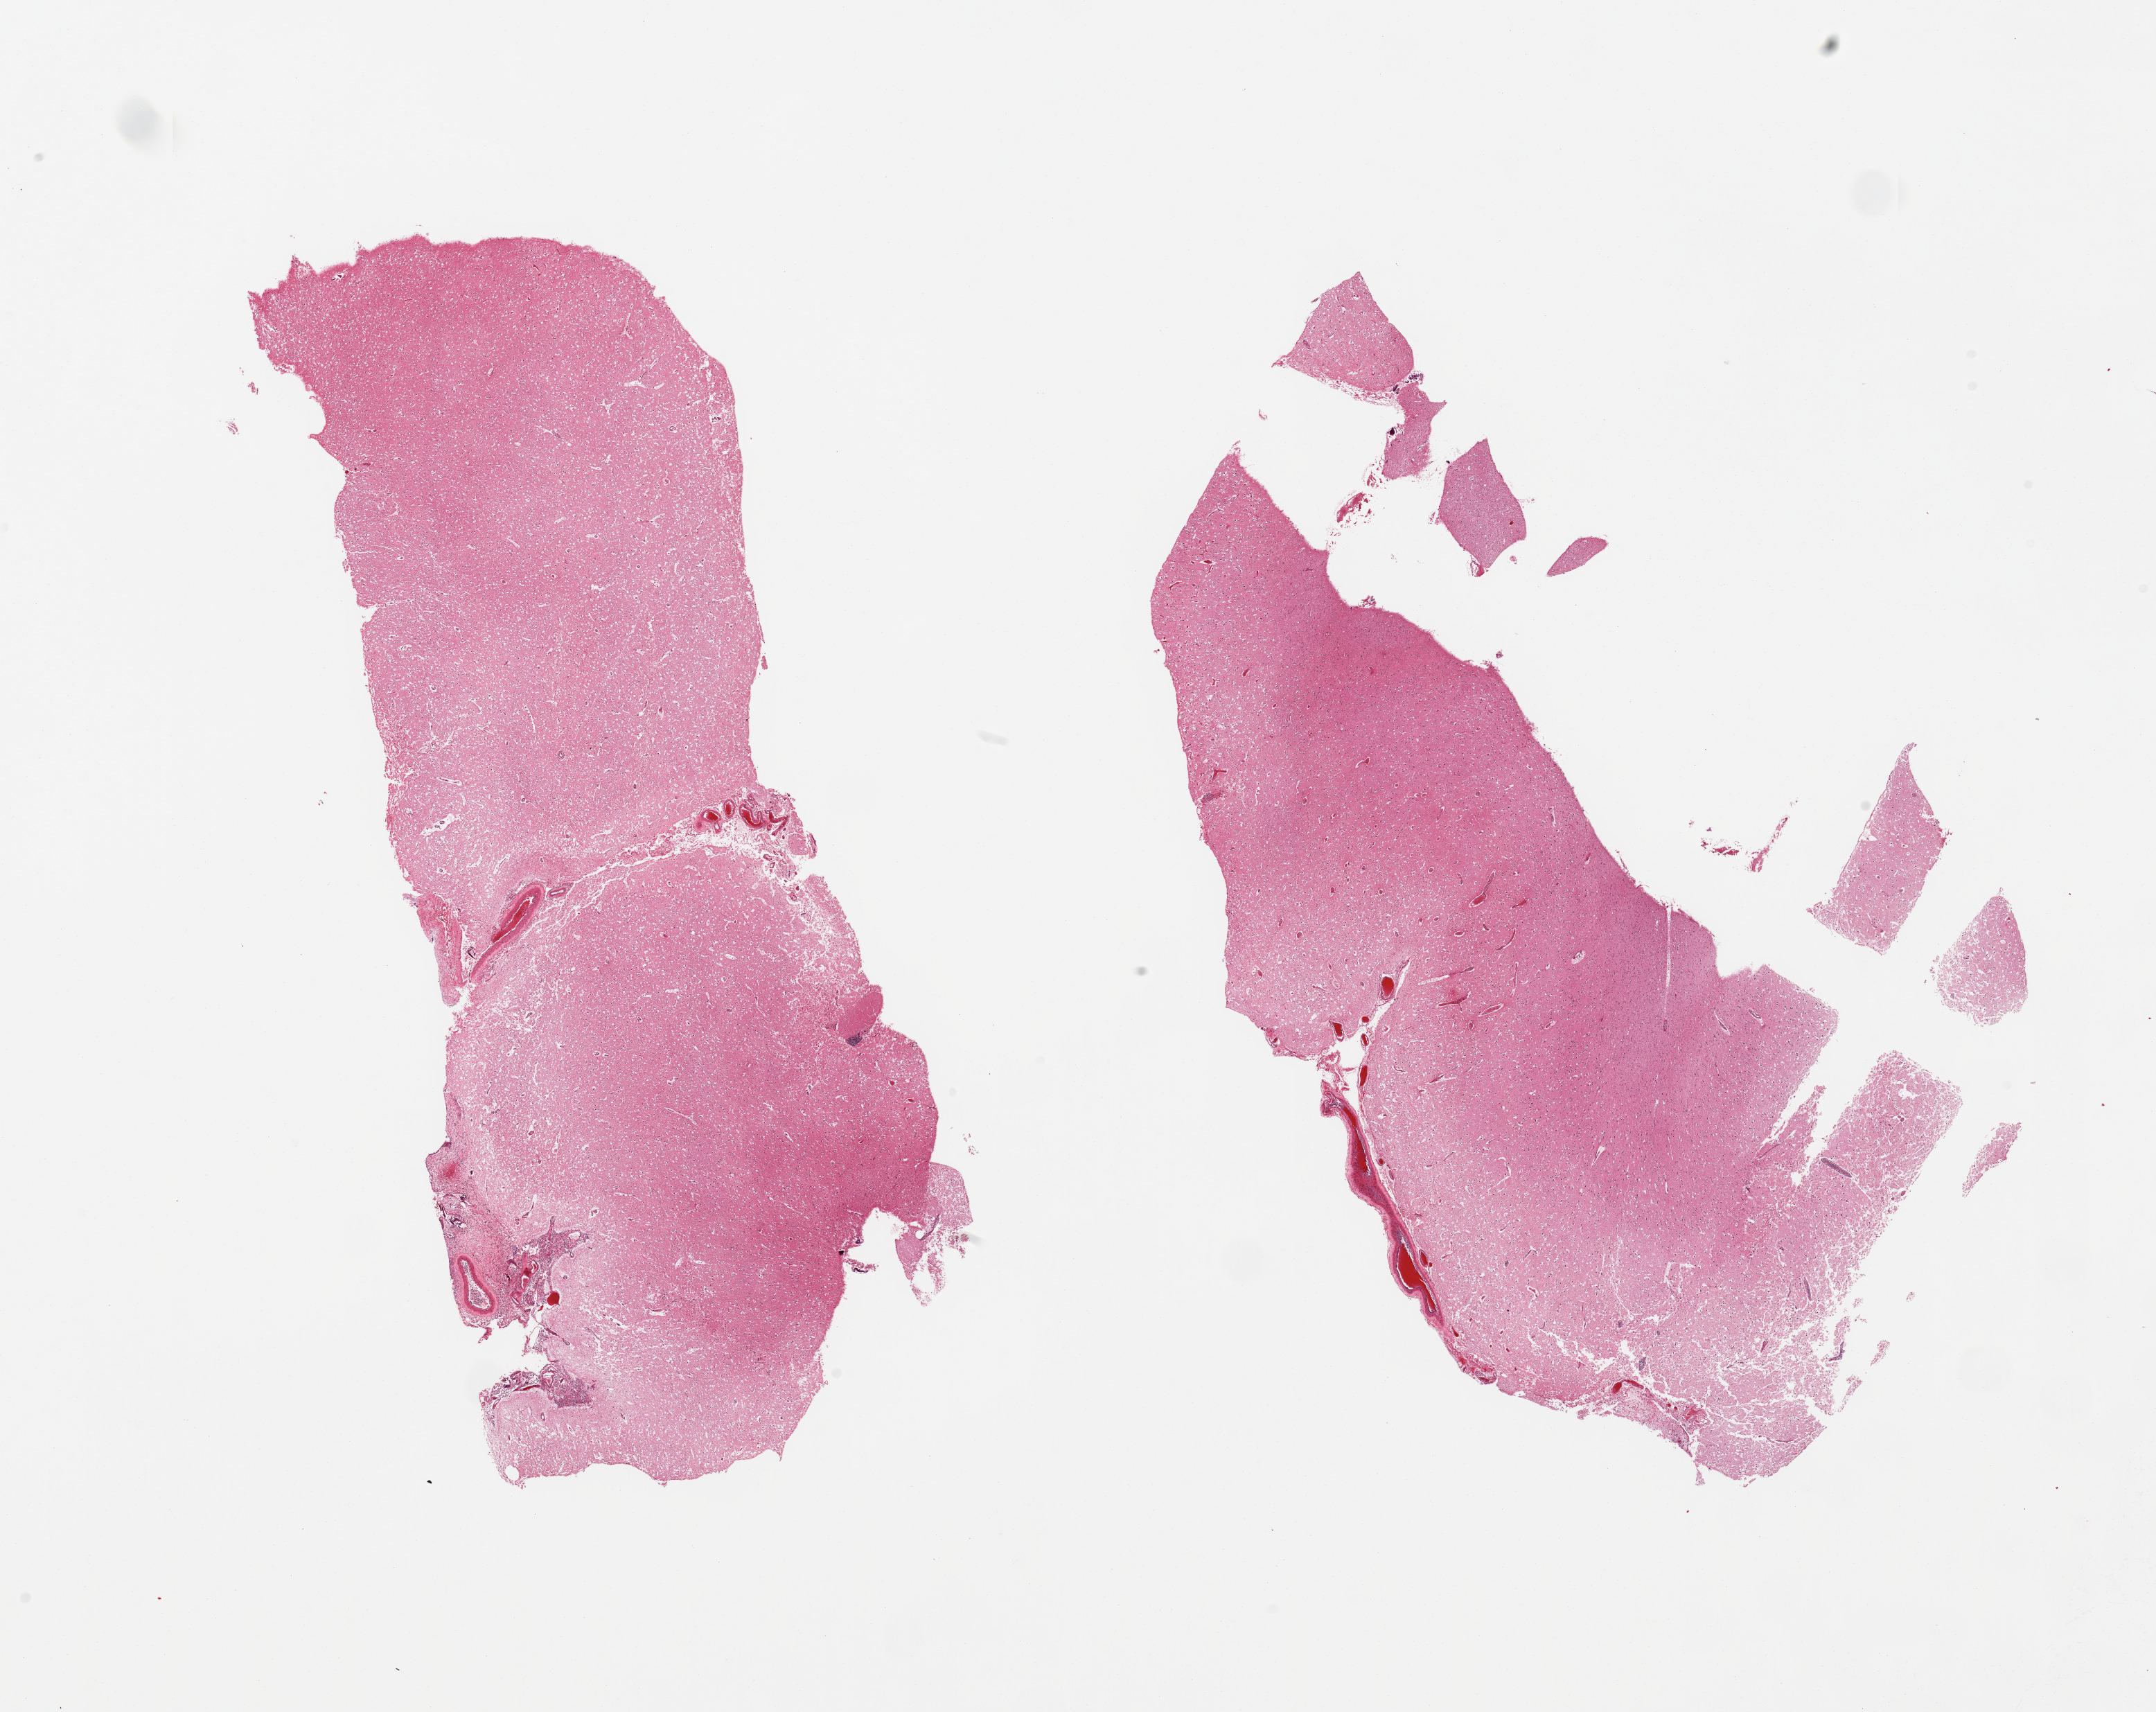
Hematoxylin and eosin (H&E) whole-slide image — whole scanned area (about 24.6 x 19.5 mm) shown as a low-resolution overview. PAXgene-fixed, paraffin-embedded tissue. Sampled site (target tissue): cerebral cortex. Tissue donor sample. Donor: male.
* pathologist's review note for this sample: 2 pieces, no abnormalities